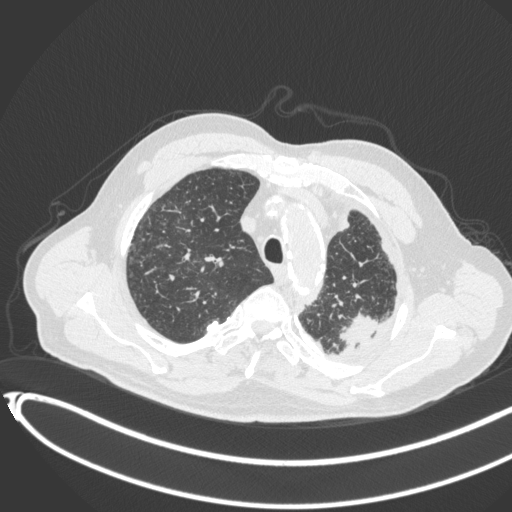
Chest CT, one axial slice. Slice 344 of 451 in the series (ordered by position). Reconstruction kernel B31f. Lung window (W 1500 / L -600 HU). 512 × 512 image matrix, field of view 400 × 400 mm. Male patient, age 78 years. Case-level facts recorded for this patient, not image findings: clinical TNM (as recorded): T1c N0 M1.
Outlined on this slice (bounding box drawn by a radiologist):
- lung tumour (recorded histology: adenocarcinoma): box from (x=337, y=309) to (x=383, y=351) px